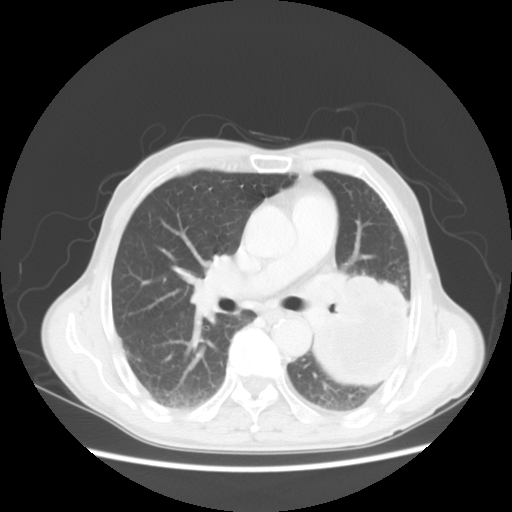
Chest CT, one axial slice. Slice 29 of 51 in the series (ordered by position). 120 kVp. Lung window (W 1500 / L -600 HU). 5 mm slice thickness. 512 × 512 image matrix, field of view 360 × 360 mm. Patient: male, 64 years. From the clinical record (not read from this slice): clinical TNM (as recorded): T4 N0 M0; histopathological grade: G2-3.
Outlined on this slice (bounding box drawn by a radiologist):
- lung tumour (recorded histology: squamous cell carcinoma): bounding box <306,265,439,414> (left, top, right, bottom; pixels)